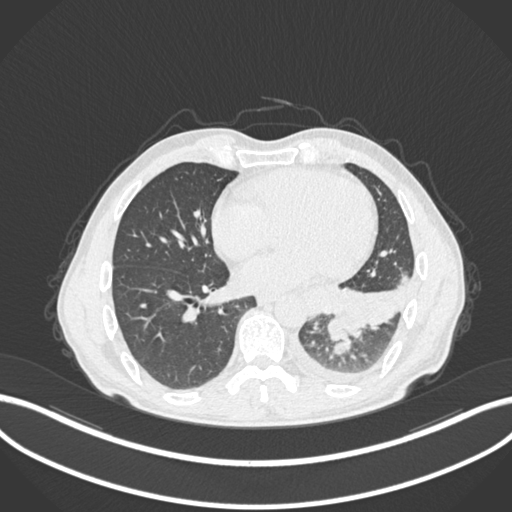
Chest CT, one axial slice. Slice 95 of 222 in the series (ordered by position). Lung window (W 1500 / L -600 HU). 1 mm slice thickness. 512 × 512 image matrix, field of view 400 × 400 mm. Male patient, age 47 years. Case-level facts recorded for this patient, not image findings: clinical TNM (as recorded): T3 N1 M1c.
Annotated regions visible in this slice (rectangle marked by the reading radiologist):
- lung tumour (recorded histology: small cell carcinoma): bounding box <326,312,348,342> (left, top, right, bottom; pixels)